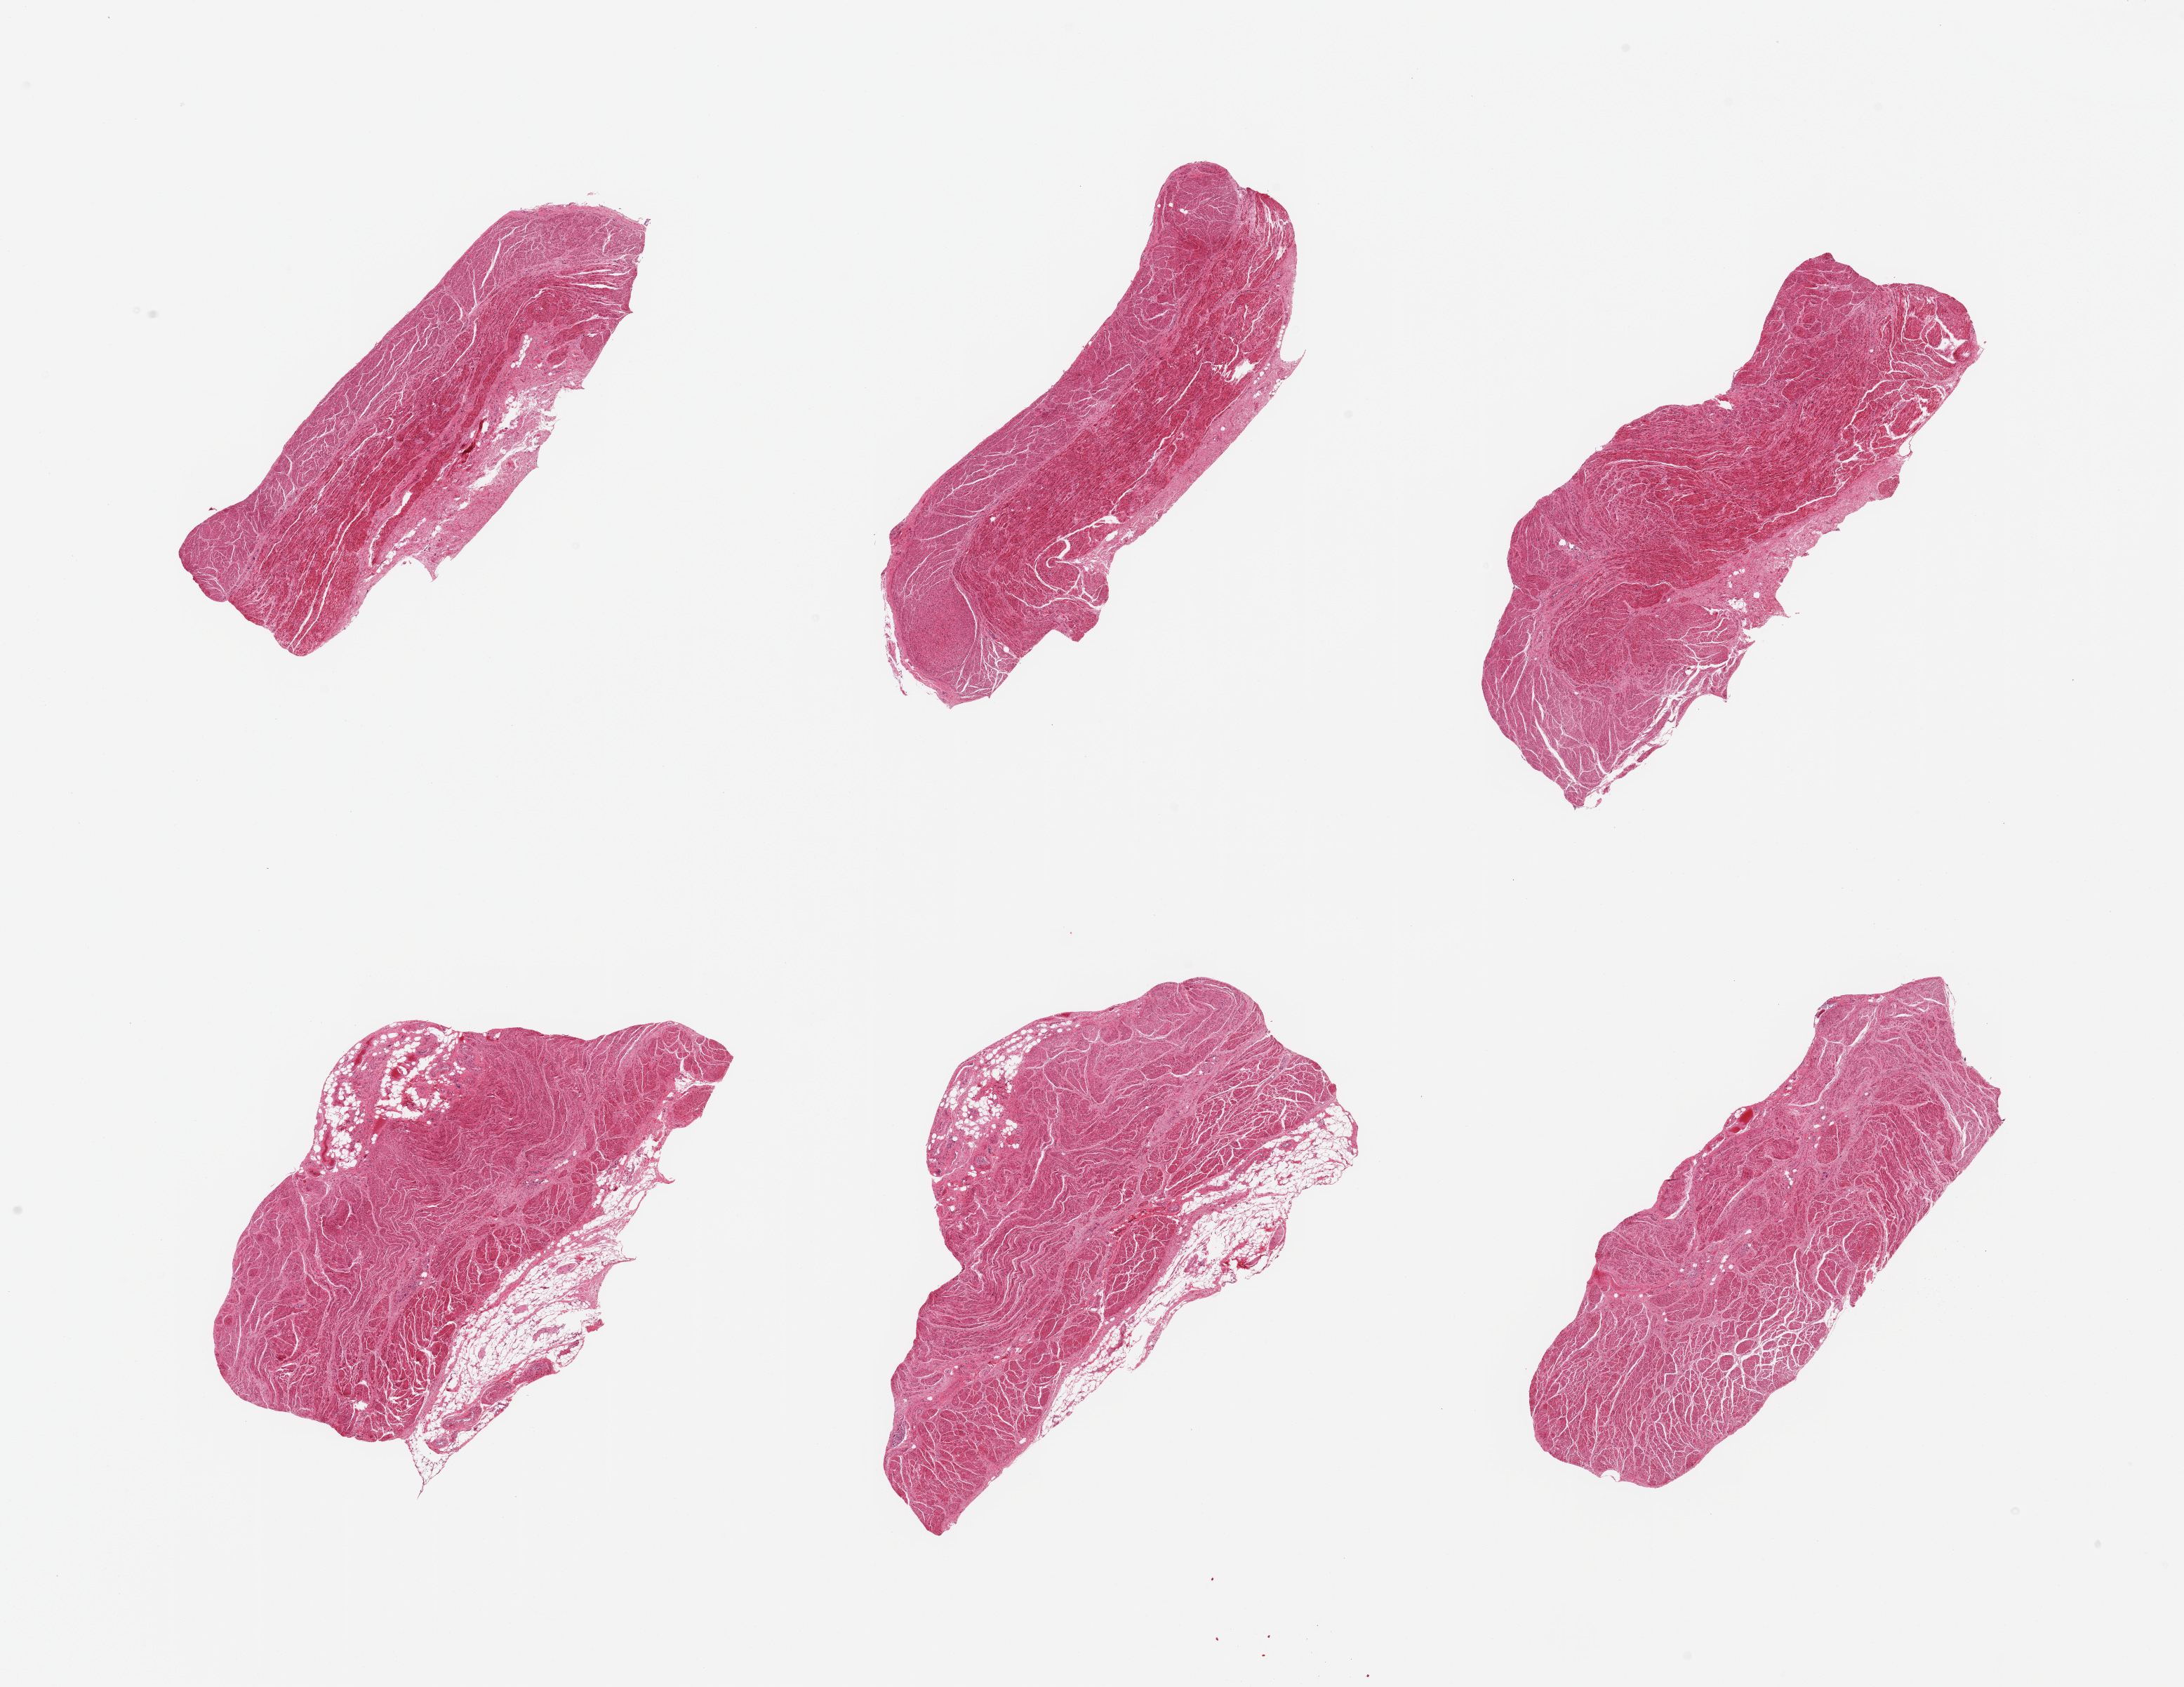
Whole-slide image, haematoxylin and eosin stain — whole scanned area (about 24.6 x 19.0 mm, from a 20x scan) shown as a low-resolution overview. PAXgene-fixed paraffin-embedded (PFPE) section. Sampled site (target tissue): gastroesophageal junction. Tissue donor sample. Donor sex: male.
Reviewer comment on this tissue sample: 6 pieces, confirmed target muscularis.